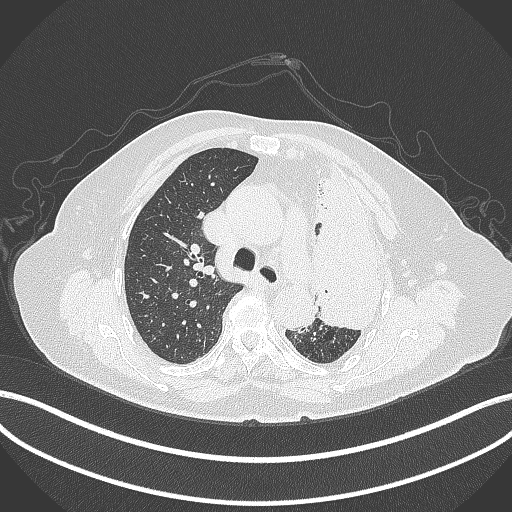
Chest CT, one axial slice. Position 272 of 399 along the scan axis. Lung window (W 1500 / L -600 HU). 1 mm slice thickness. 512 × 512 image matrix. Patient: female, 75 years. From the clinical record (not read from this slice): clinical TNM (as recorded): T3 N3 M1.
Annotated regions visible in this slice (rectangle marked by the reading radiologist):
- lung tumour (recorded histology: adenocarcinoma): bounding box (x1, y1, x2, y2) in pixels: (308, 159, 392, 339)